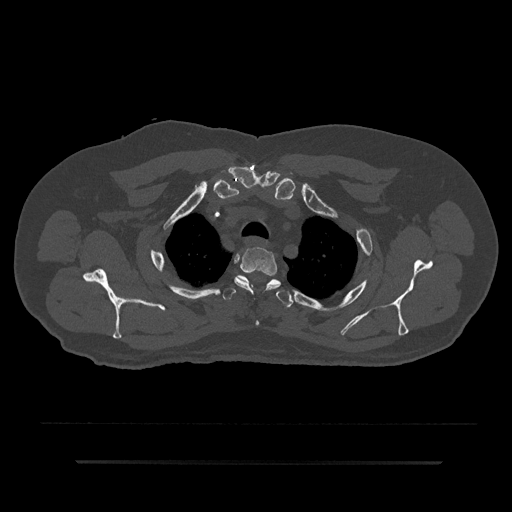
CT including the spine, one axial slice. Position 684 of 797 along the scan axis. Reconstruction kernel Br40s/3. Bone window (W 1800 / L 400 HU). 0.5 mm slice thickness. 512 × 512 image matrix, field of view 464 × 464 mm. Male patient, age 59 years. Case-level facts recorded for this patient, not image findings: primary cancer: bile ducts; vertebrae with lytic lesions (as recorded): T10.
Structures marked on this image (semi-automatically segmented with operator editing):
- T2 vertebra: bounding box [x1, y1, x2, y2] px = [234, 247, 281, 325]
- T3 vertebra: [223, 275, 293, 308]